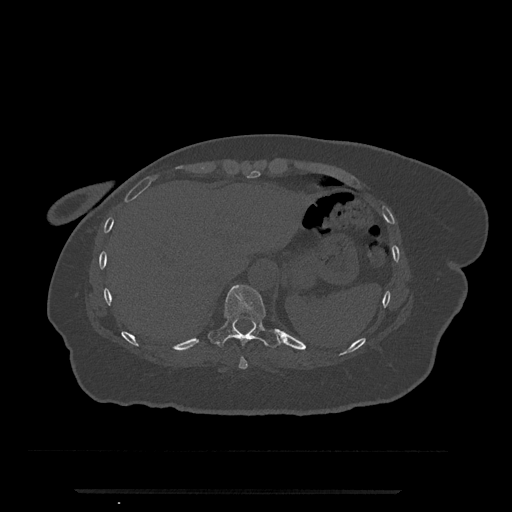
CT including the spine, one axial slice. Position 295 of 797 along the scan axis. Reconstruction kernel Br40s/3. 120 kVp. Bone window (W 1800 / L 400 HU). 0.5 mm slice thickness. 512 × 512 image matrix, field of view 440 × 440 mm. Female patient, age 51 years. Case-level facts recorded for this patient, not image findings: primary cancer: neuro; vertebrae with lytic lesions (as recorded): T8.
Structures marked on this image (semi-automatic segmentation, software-assisted and operator-edited):
- T10 vertebra: bounding box [x1, y1, x2, y2] px = [210, 285, 280, 348]
- T9 vertebra: [238, 356, 248, 369]